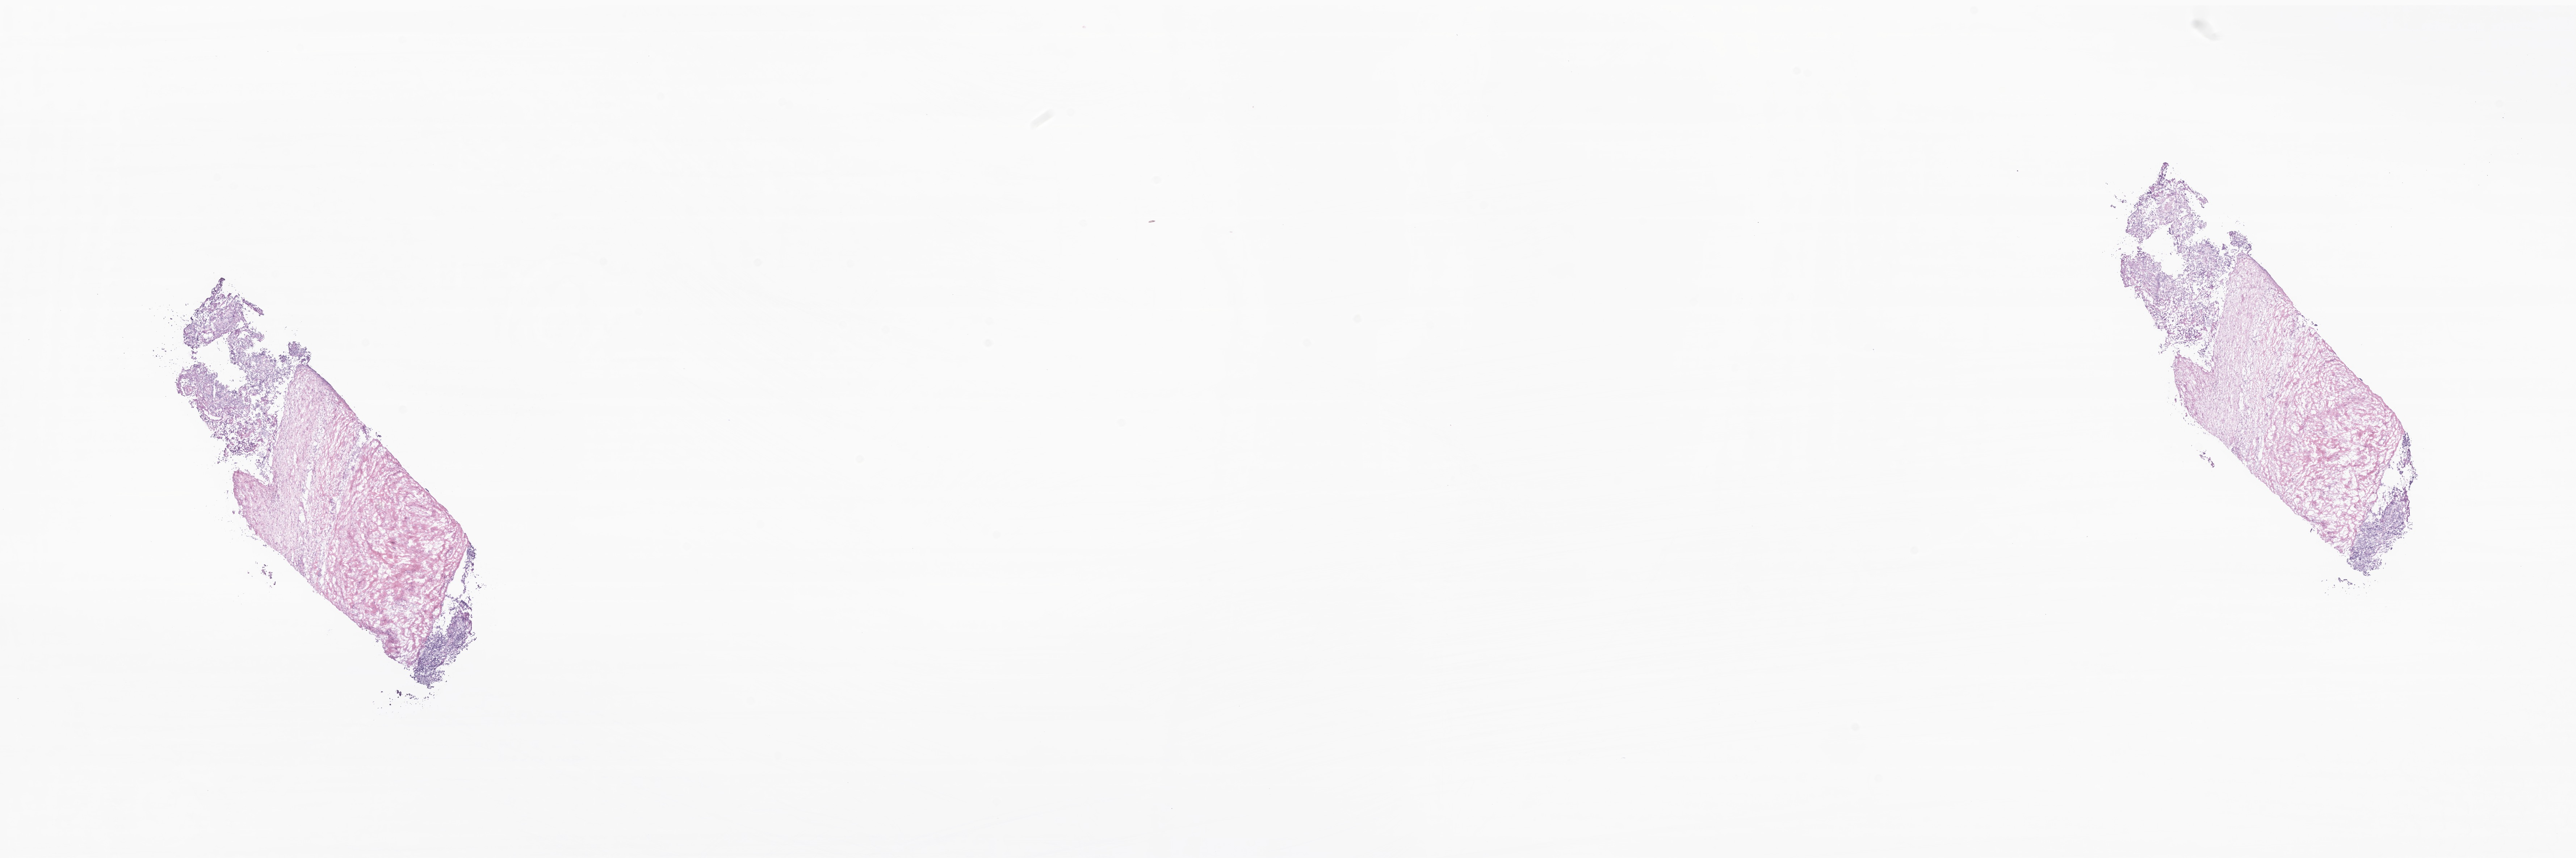
Haematoxylin and eosin whole-slide image of tumor tissue from the abdomen — low-resolution overview of the scanned area, about 30.0 x 10.0 mm. Cryosection (OCT / tissue freezing medium). Female patient, age 81 months.
Recorded diagnosis: Neuroblastoma, NOS.